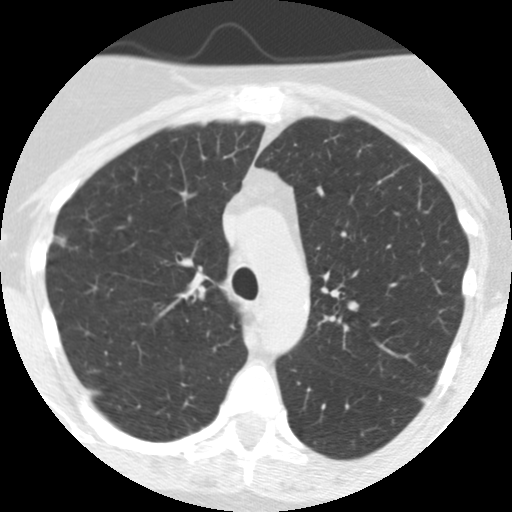
Chest CT (low-dose screening protocol), one axial image. Baseline screening round. Lung window (W 1500 / L -600 HU). Slice 174 of 249 in the series. Female, age 55 years at enrolment. Current smoker at enrolment.
• Lesion marked by an expert reader, bounding box (x1, y1, x2, y2) in pixels: (33, 219, 82, 271).
• Reader record for this screening exam (exam-level; its link to the box is not recorded): non-calcified nodule or mass ≥4 mm, right upper lobe, 7 × 7 mm, spiculated (stellate) margins, soft tissue attenuation.
• Lung cancer was diagnosed 1018 days after this screen (after the third annual screen): bronchiolo-alveolar adenocarcinoma, NOS, right upper lobe, moderately differentiated (G2), stage IIA (AJCC 6th edition), 13 mm at pathology.